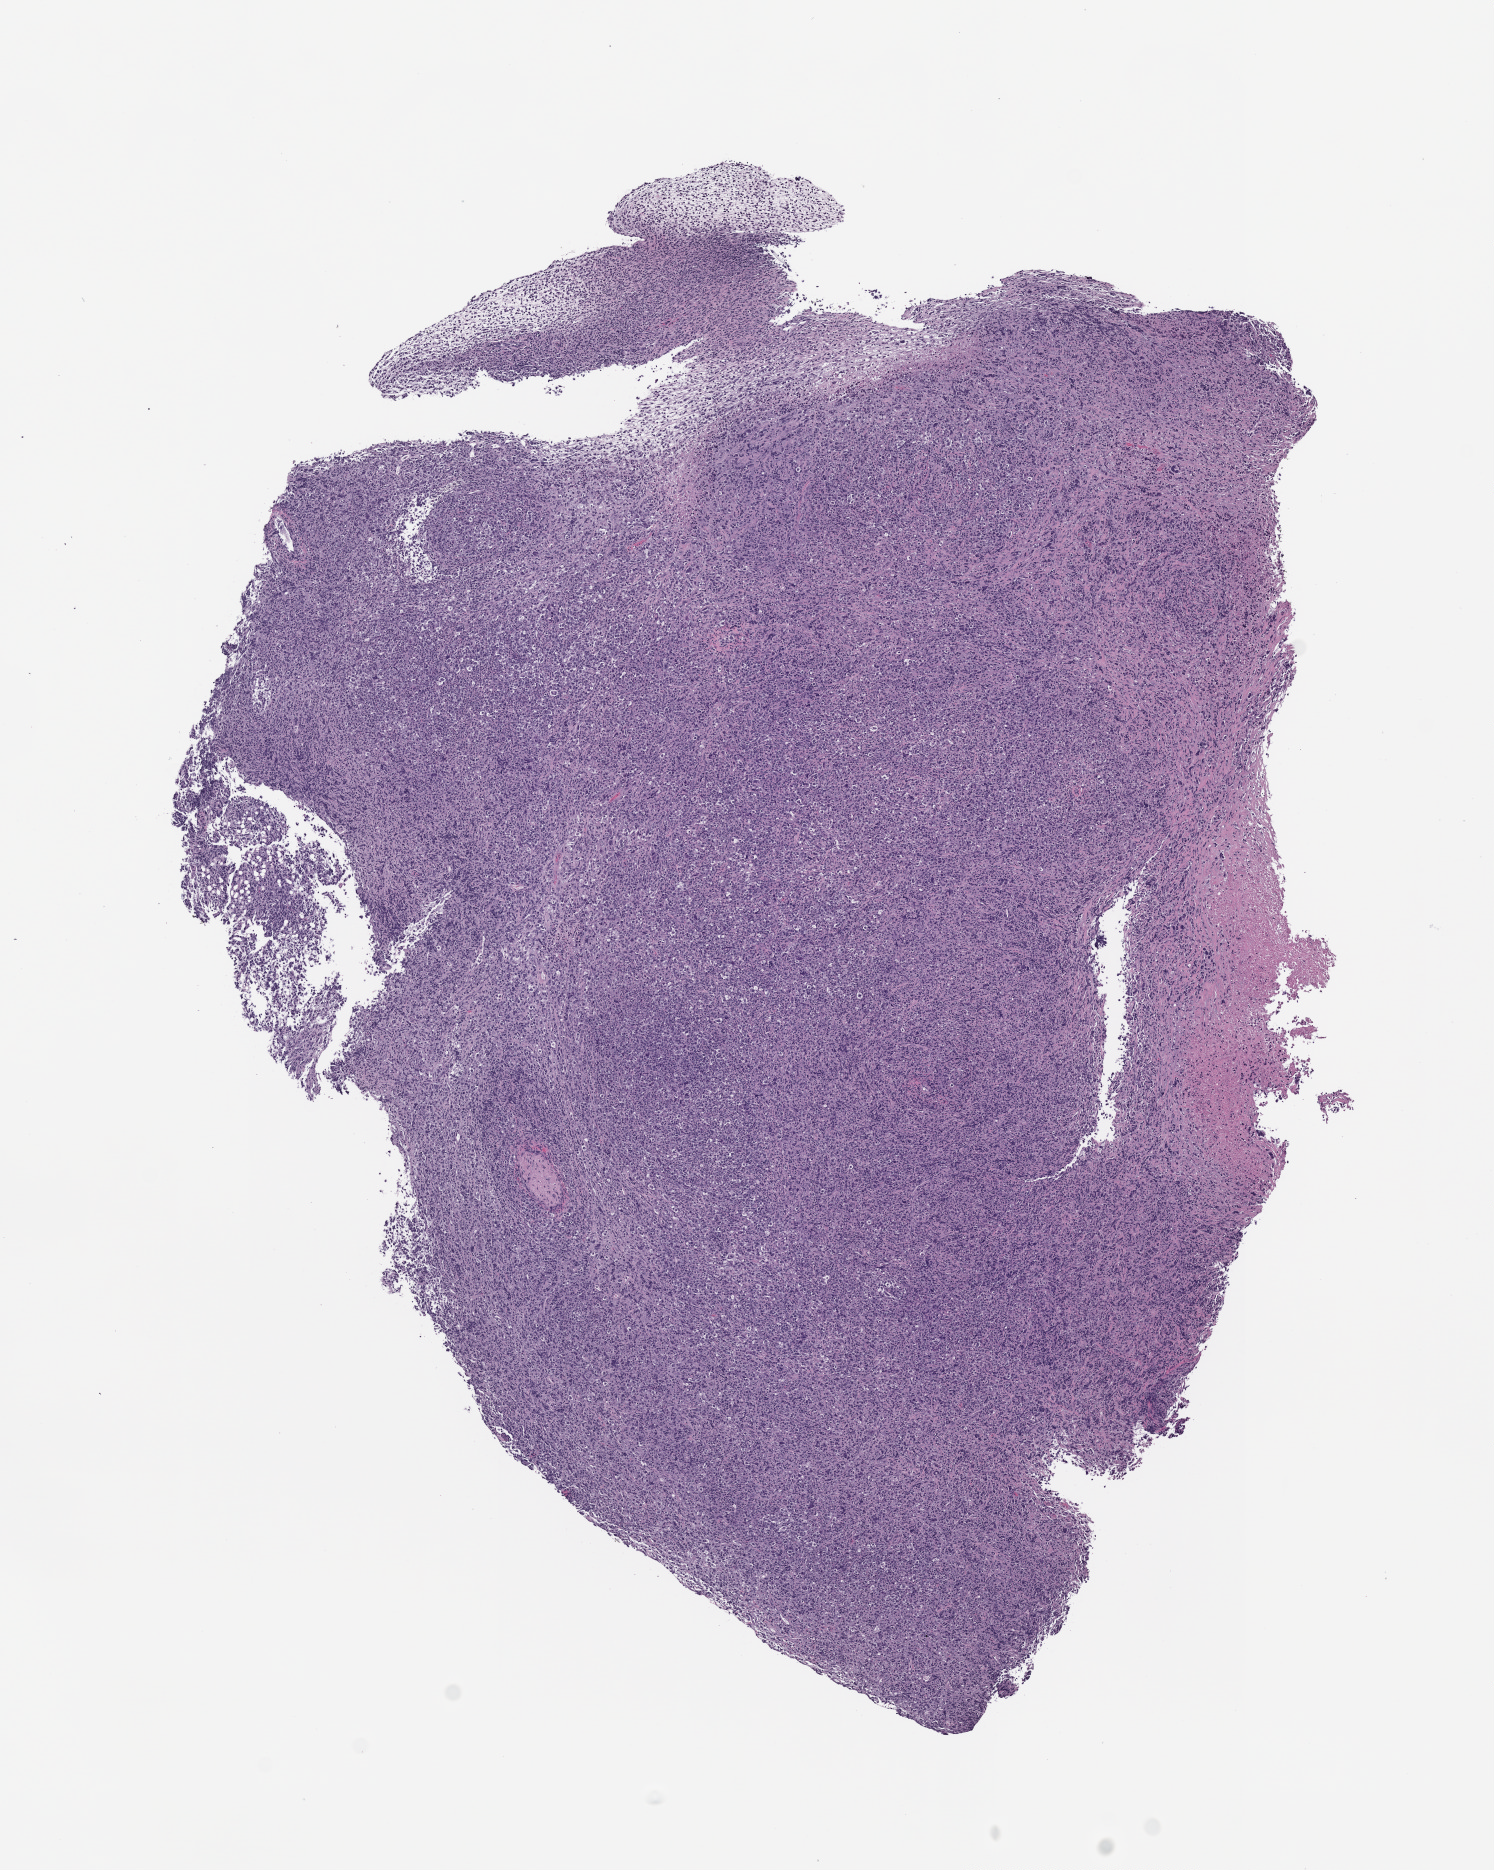
Haematoxylin and eosin whole-slide image of a patient-derived xenograft (PDX) tumor grown in a mouse — a low-resolution overview of the entire scanned area, about 6.0 x 7.5 mm.
Specimen: FFPE section.